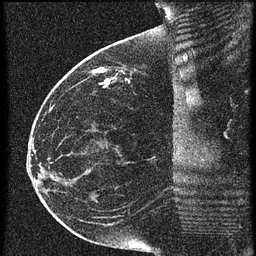
Breast MRI (dynamic contrast-enhanced), one sagittal slice; slice 24 of 60 in the series (ordered by position); 3 images stored at this slice position (order not interpretable as contrast timing); 1.5 T; TE 4.2 ms, TR 20.4 ms; 256 × 256 image matrix, field of view 200 × 200 mm. Female patient, age 35 years. From the clinical record (not read from this slice): setting: breast cancer imaged before/during neoadjuvant chemotherapy; receptor status: HR-positive, HER2-negative.
Outlined on this slice (semi-automatic segmentation, software-assisted and operator-edited):
- analysis volume of interest (the breast-tissue region the enhancement analysis was run in; not a lesion): bounding box (x1, y1, x2, y2) in pixels: (84, 50, 179, 97)
- tumour enhancement mask (voxels above the 90 % enhancement threshold inside the analysis volume of interest): (96, 68, 109, 85)